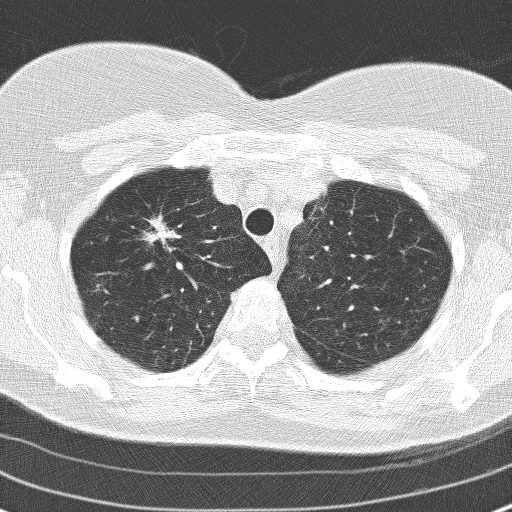
Axial slice from a low-dose chest CT screening exam; second annual screen; lung window (W 1500 / L -600 HU); 120 kVp; slice 33 of 160 in the series; 512 × 512 image matrix, field of view 313 × 313 mm. Female, age 60 years at enrolment. Former smoker at enrolment.
• Expert reader's lesion annotation, bounding box (x1, y1, x2, y2) in pixels: (125, 207, 179, 257).
• Screening reader's record for this exam (one nodule recorded; not confirmed to be the boxed lesion): non-calcified nodule or mass ≥4 mm, right upper lobe, 17 × 15 mm, spiculated (stellate) margins, soft tissue attenuation, pre-existing on the prior screen: yes; interval growth: yes.
• Later outcome: lung cancer diagnosed 78 days after this screen — adenocarcinoma, NOS, right upper lobe, moderately differentiated (G2), stage IA (AJCC 6th edition), 23 mm at pathology.